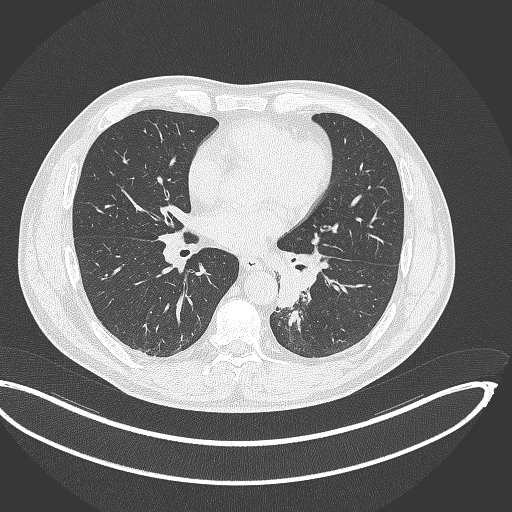
Chest CT, one axial slice; position 166 of 362 along the scan axis; 120 kVp; lung window (W 1500 / L -600 HU); 1 mm slice thickness; 512 × 512 image matrix, field of view 442 × 442 mm. Patient: male, 50 years. Case-level facts recorded for this patient, not image findings: clinical TNM (as recorded): T2a N3 M0.
Annotated regions visible in this slice (bounding box drawn by a radiologist):
- lung tumour (recorded histology: squamous cell carcinoma): box from (x=278, y=262) to (x=318, y=309) px